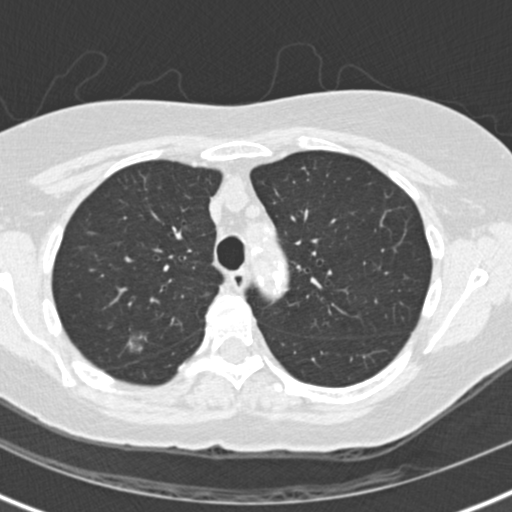
Low-dose screening chest CT, axial slice, baseline screening round, lung window (W 1500 / L -600 HU), 2 mm slice thickness, standard (soft-tissue) reconstruction kernel (B30f), slice 44 of 147 in the series. Female, age 72 years at enrolment. Current smoker at enrolment.
- Lesion marked by an expert reader, bounding box <107,323,165,372> (left, top, right, bottom; pixels).
- Reader record for this screening exam (exam-level; its link to the box is not recorded): non-calcified nodule or mass ≥4 mm, right upper lobe, 11 × 11 mm, poorly defined margins, ground glass attenuation.
- Later outcome: lung cancer diagnosed 75 days after this screen — bronchiolo-alveolar adenocarcinoma, NOS, right upper lobe, well differentiated (G1), stage IA (AJCC 6th edition), 23 mm at pathology.